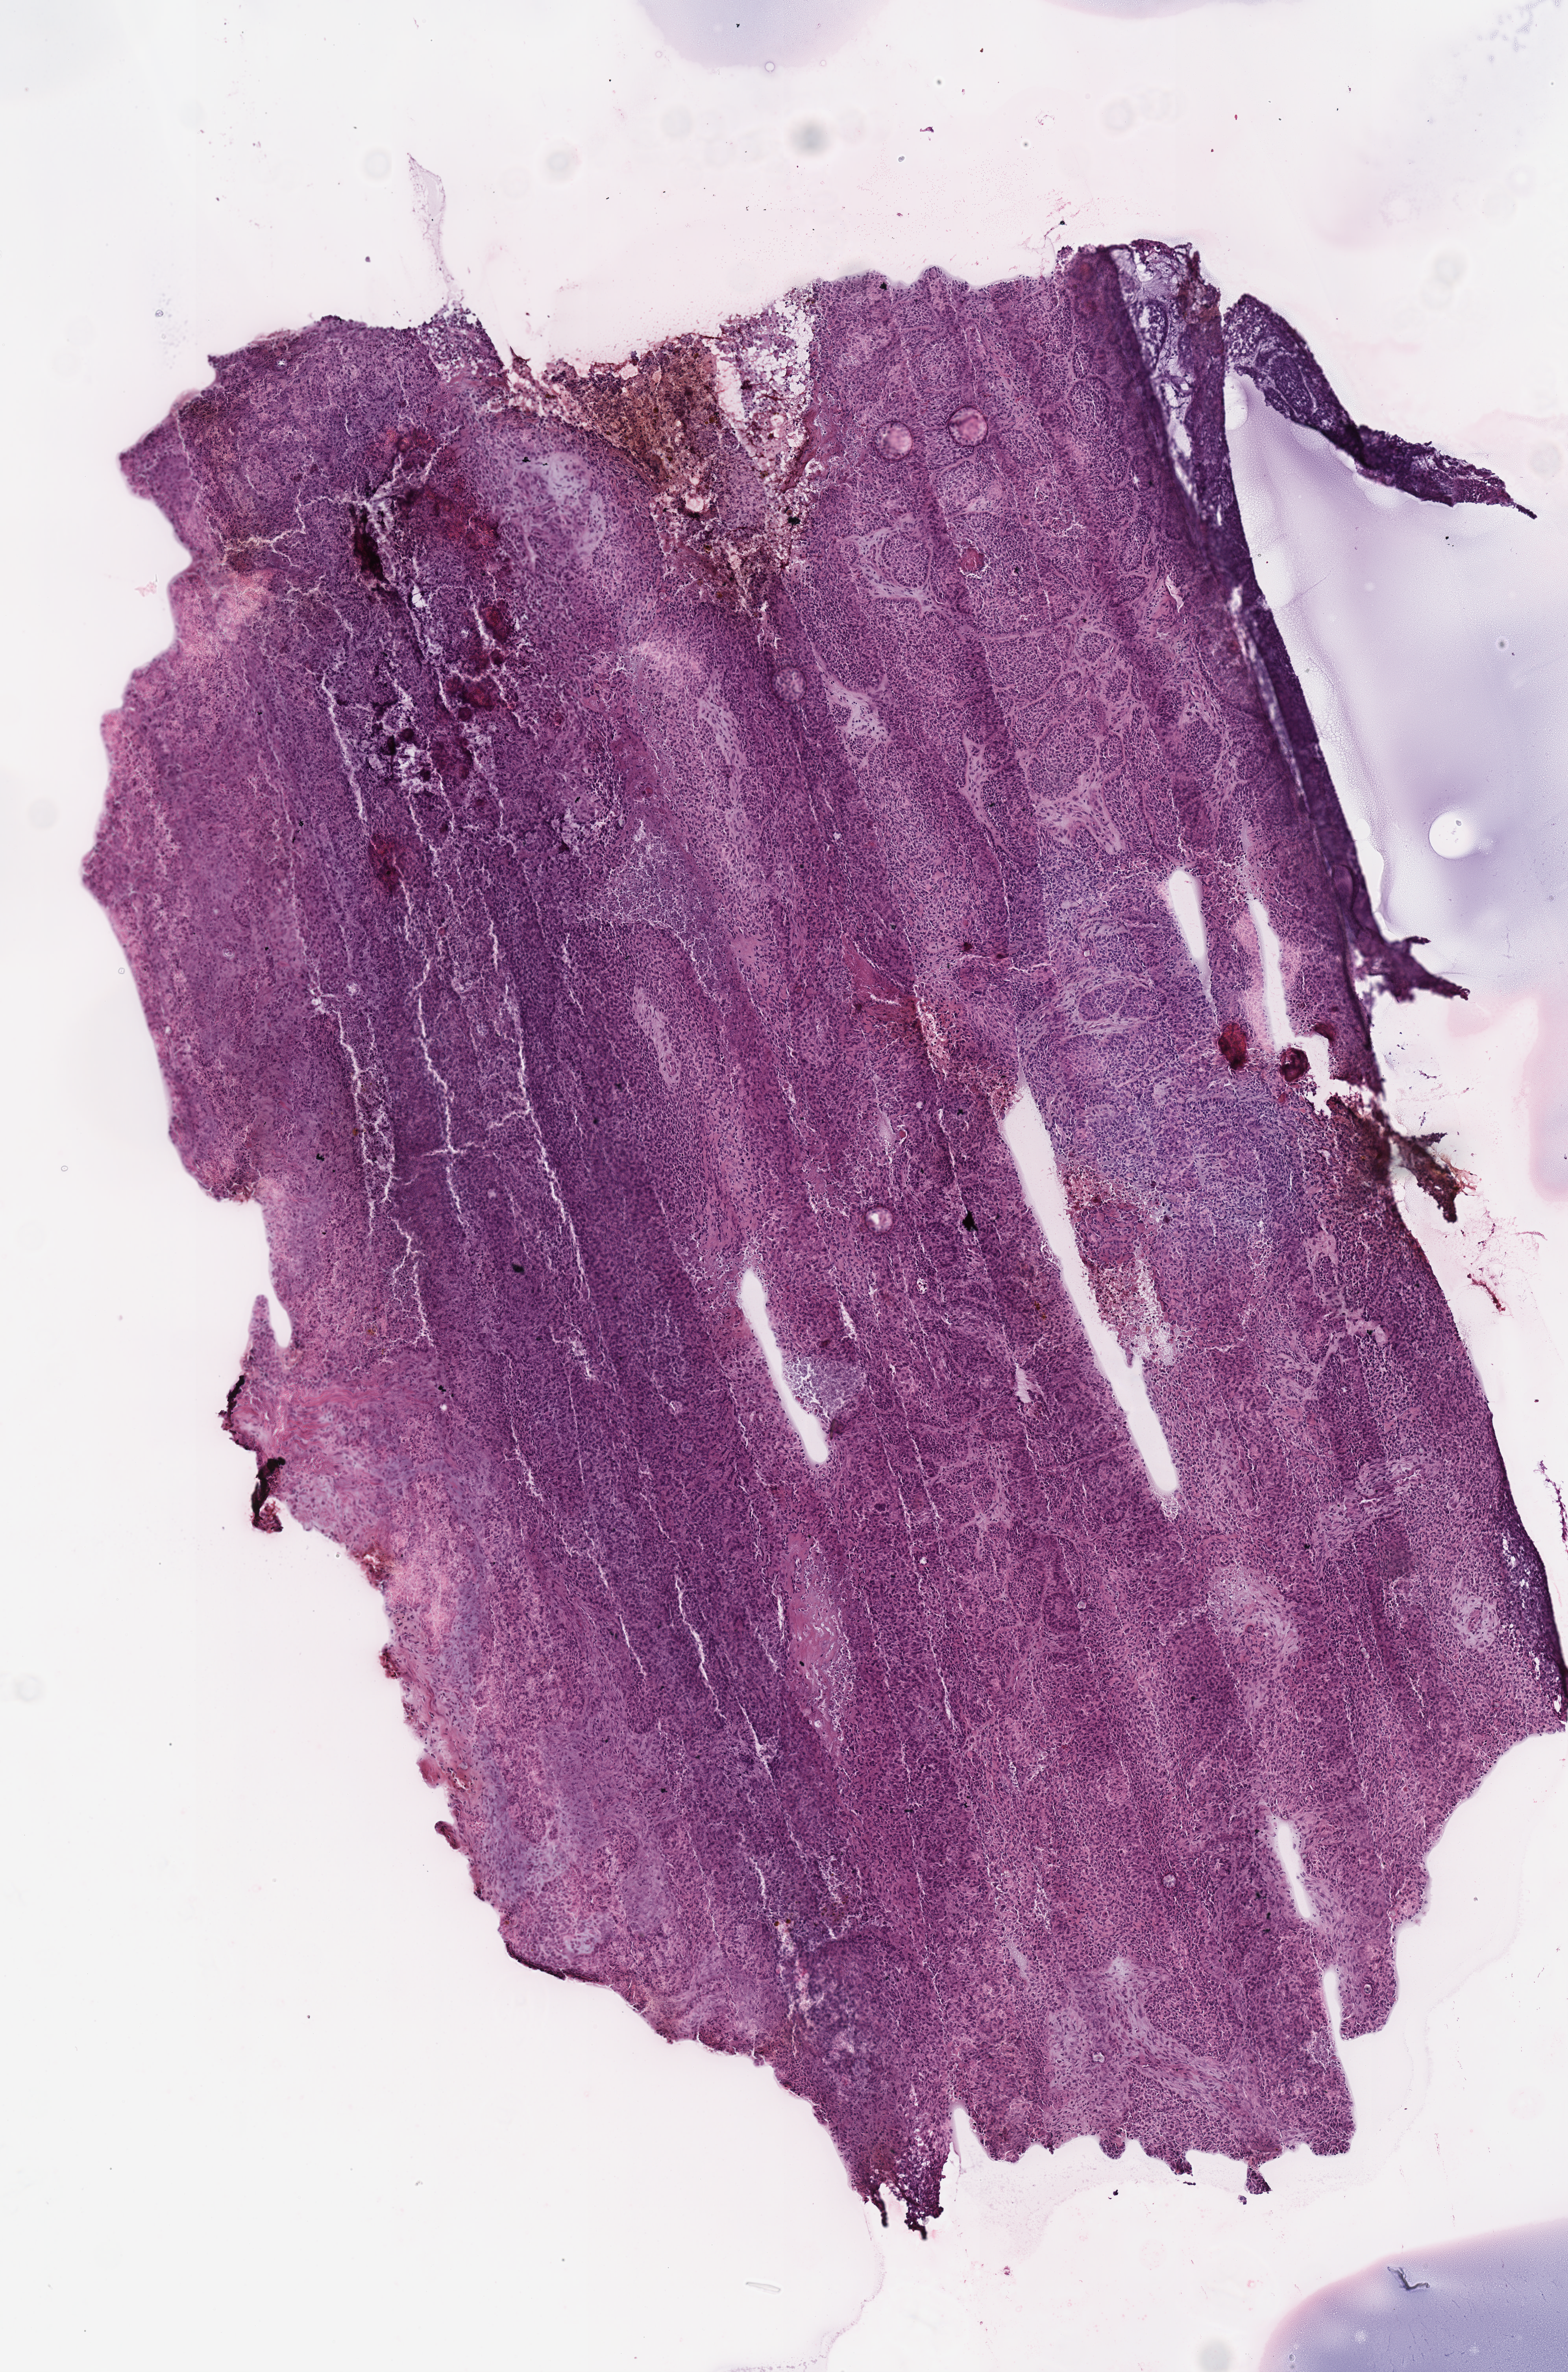
Digitized Hematoxylin and eosin (H&E) stained tissue section (whole slide) — a low-resolution overview of the entire scanned area, about 3.9 x 5.9 mm (slide scanned at 40x); frozen section from the top of the tissue portion; lung, primary tumour sample. Male, age 70 years at initial diagnosis. Slide review estimates, as recorded: tumour cells 88%, tumour nuclei 80%, normal cells 0%, stromal cells 5%, necrosis 7%. Infiltration values recorded for this section: lymphocyte infiltration 15%.
• pathologic diagnosis: Squamous cell carcinoma, NOS (lower lobe, lung)
• AJCC pathologic stage: IIA (7th edition)
• TNM: T2b N0 M0
• laterality: right